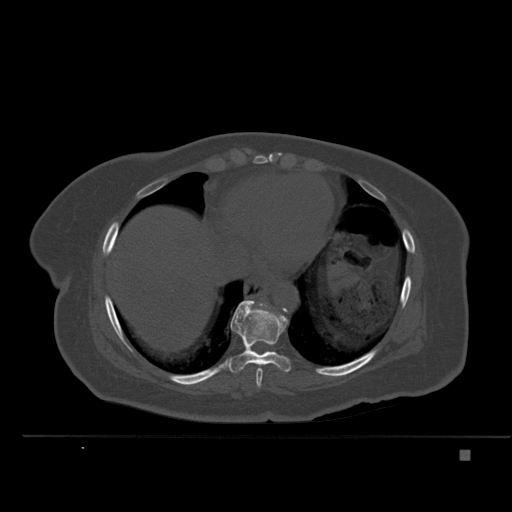
CT including the spine, one axial slice. Position 298 of 477 along the scan axis. Bone window (W 1800 / L 400 HU). 1.5 mm slice thickness. 512 × 512 image matrix. Female patient, age 74 years. Case-level facts recorded for this patient, not image findings: primary cancer: colon.
Outlined on this slice (semi-automatic segmentation, software-assisted and operator-edited):
- T8 vertebra: bounding box (x1, y1, x2, y2) in pixels: (256, 368, 263, 388)
- T9 vertebra: (222, 300, 291, 373)